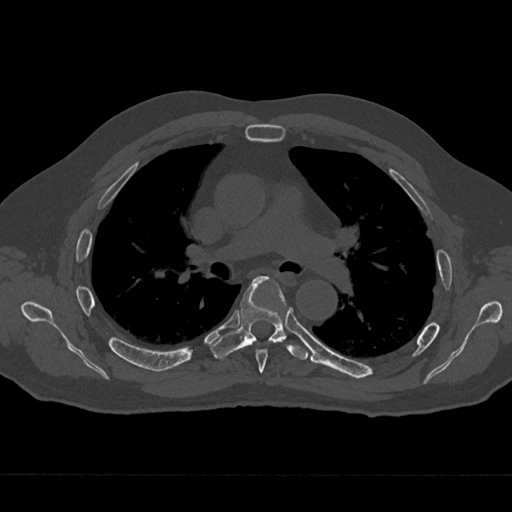
CT including the spine, one axial slice; slice 444 of 797 in the series (ordered by position); 120 kVp; bone window (W 1800 / L 400 HU); 0.5 mm slice thickness; 512 × 512 image matrix, field of view 377 × 377 mm. Patient: male, 75 years. From the clinical record (not read from this slice): primary cancer: renal; vertebrae with lytic lesions (as recorded): T4.
Annotated regions visible in this slice (semi-automatic segmentation, software-assisted and operator-edited):
- T5 vertebra: bounding box [x1, y1, x2, y2] px = [256, 286, 287, 373]
- T6 vertebra: [211, 276, 308, 360]